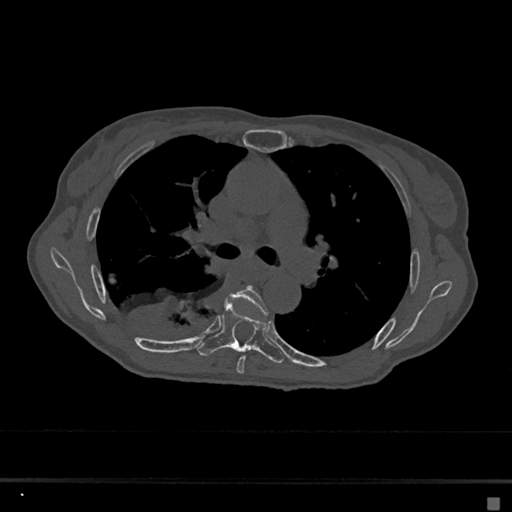
CT including the spine, one axial slice. Slice 434 of 797 in the series (ordered by position). Reconstruction kernel Br40s/3. 120 kVp. Bone window (W 1800 / L 400 HU). 0.5 mm slice thickness. 512 × 512 image matrix. Patient: female, 68 years. From the clinical record (not read from this slice): primary cancer: renal.
Outlined on this slice (semi-automatically segmented with operator editing):
- T5 vertebra: bounding box [x1, y1, x2, y2] px = [227, 285, 268, 374]
- T6 vertebra: [197, 299, 284, 364]